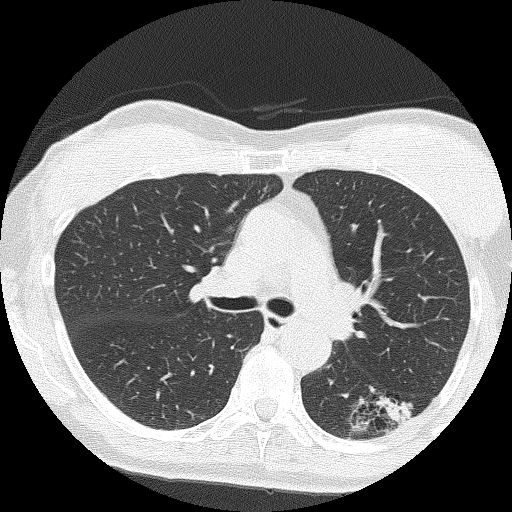
Low-dose screening chest CT, axial slice, second annual screen, lung window (W 1500 / L -600 HU). Female, age 64 years at enrolment. Former smoker at enrolment.
- Expert reader's lesion annotation, bounding box <356,382,426,439> (left, top, right, bottom; pixels).
- The screening reader recorded 3 non-calcified nodules or masses ≥4 mm on this exam; which of them this box marks is not recorded.
- Later outcome: lung cancer diagnosed 576 days after this screen — adenocarcinoma, NOS, left lower lobe, moderately differentiated (G2), stage IA (AJCC 6th edition), 17 mm at pathology.